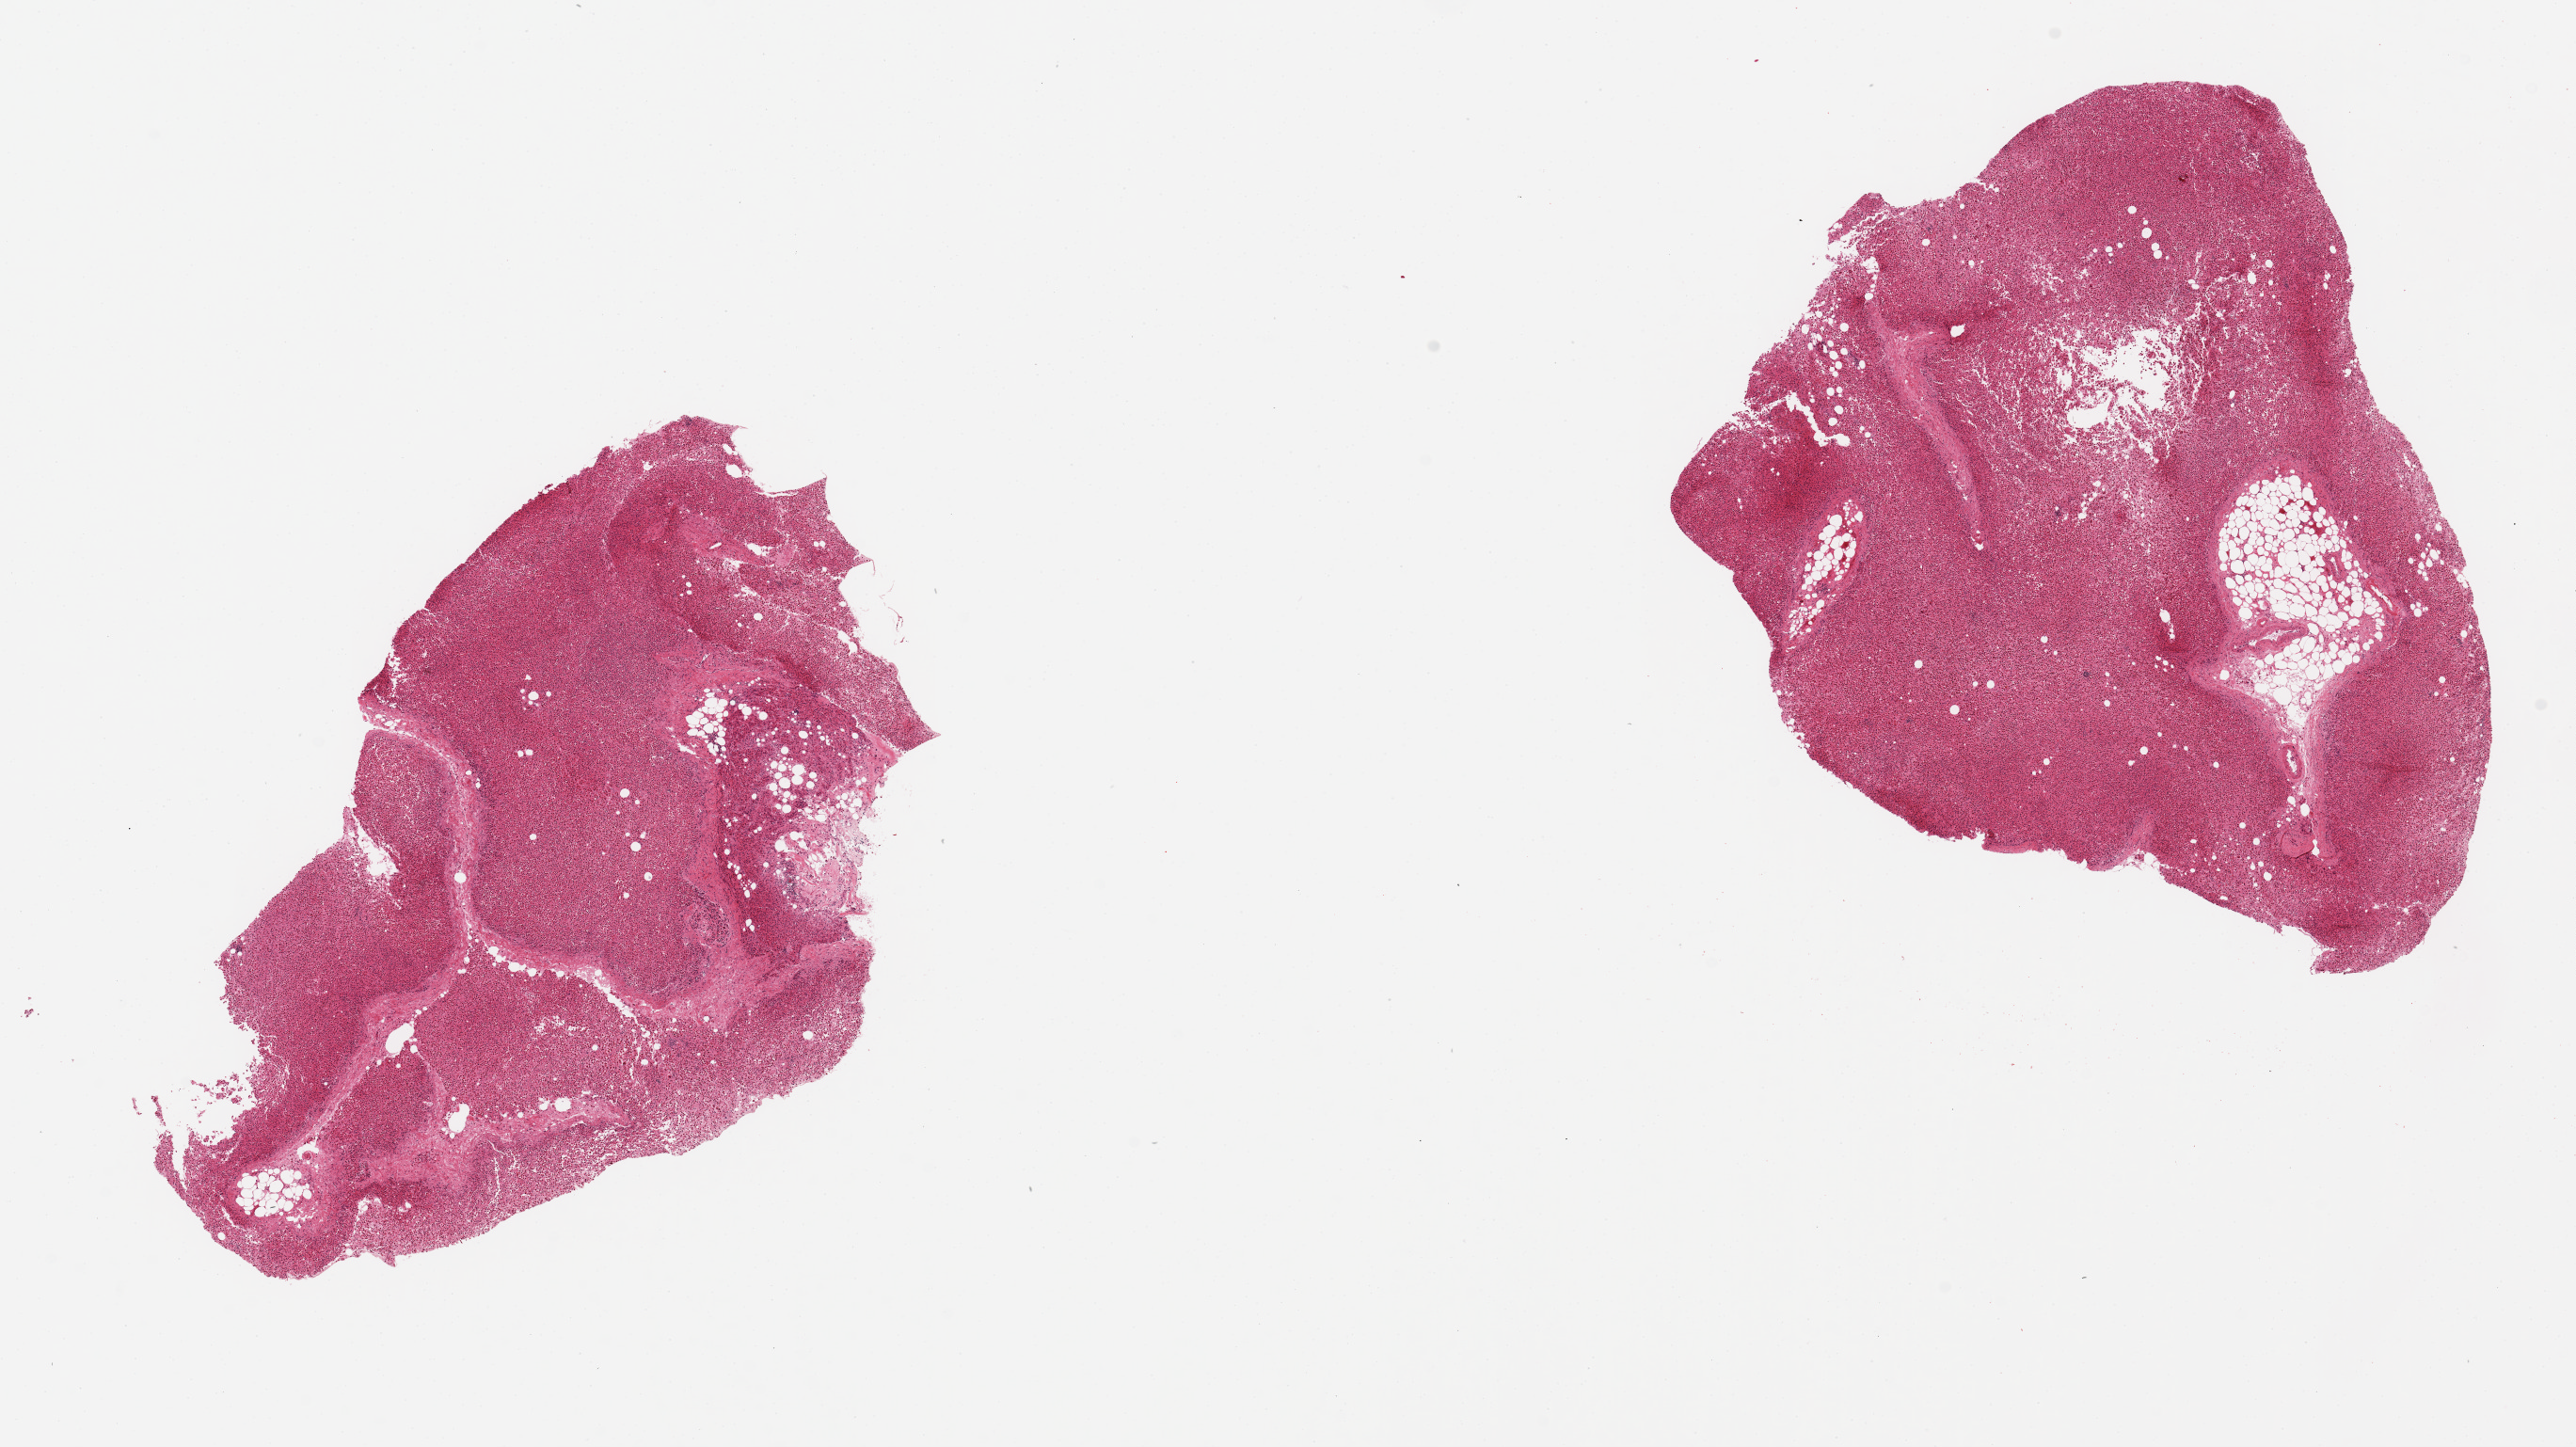
Digitized H&E-stained section, whole scanned area (about 21.7 x 12.2 mm, slide scanned at 20x) shown as a low-resolution overview, PAXgene-fixed paraffin-embedded (PFPE) section, target tissue: adrenal gland, donor tissue sample.
* pathologist's review note for this sample: 2 pieces ~7x6mm, badly autolyzed